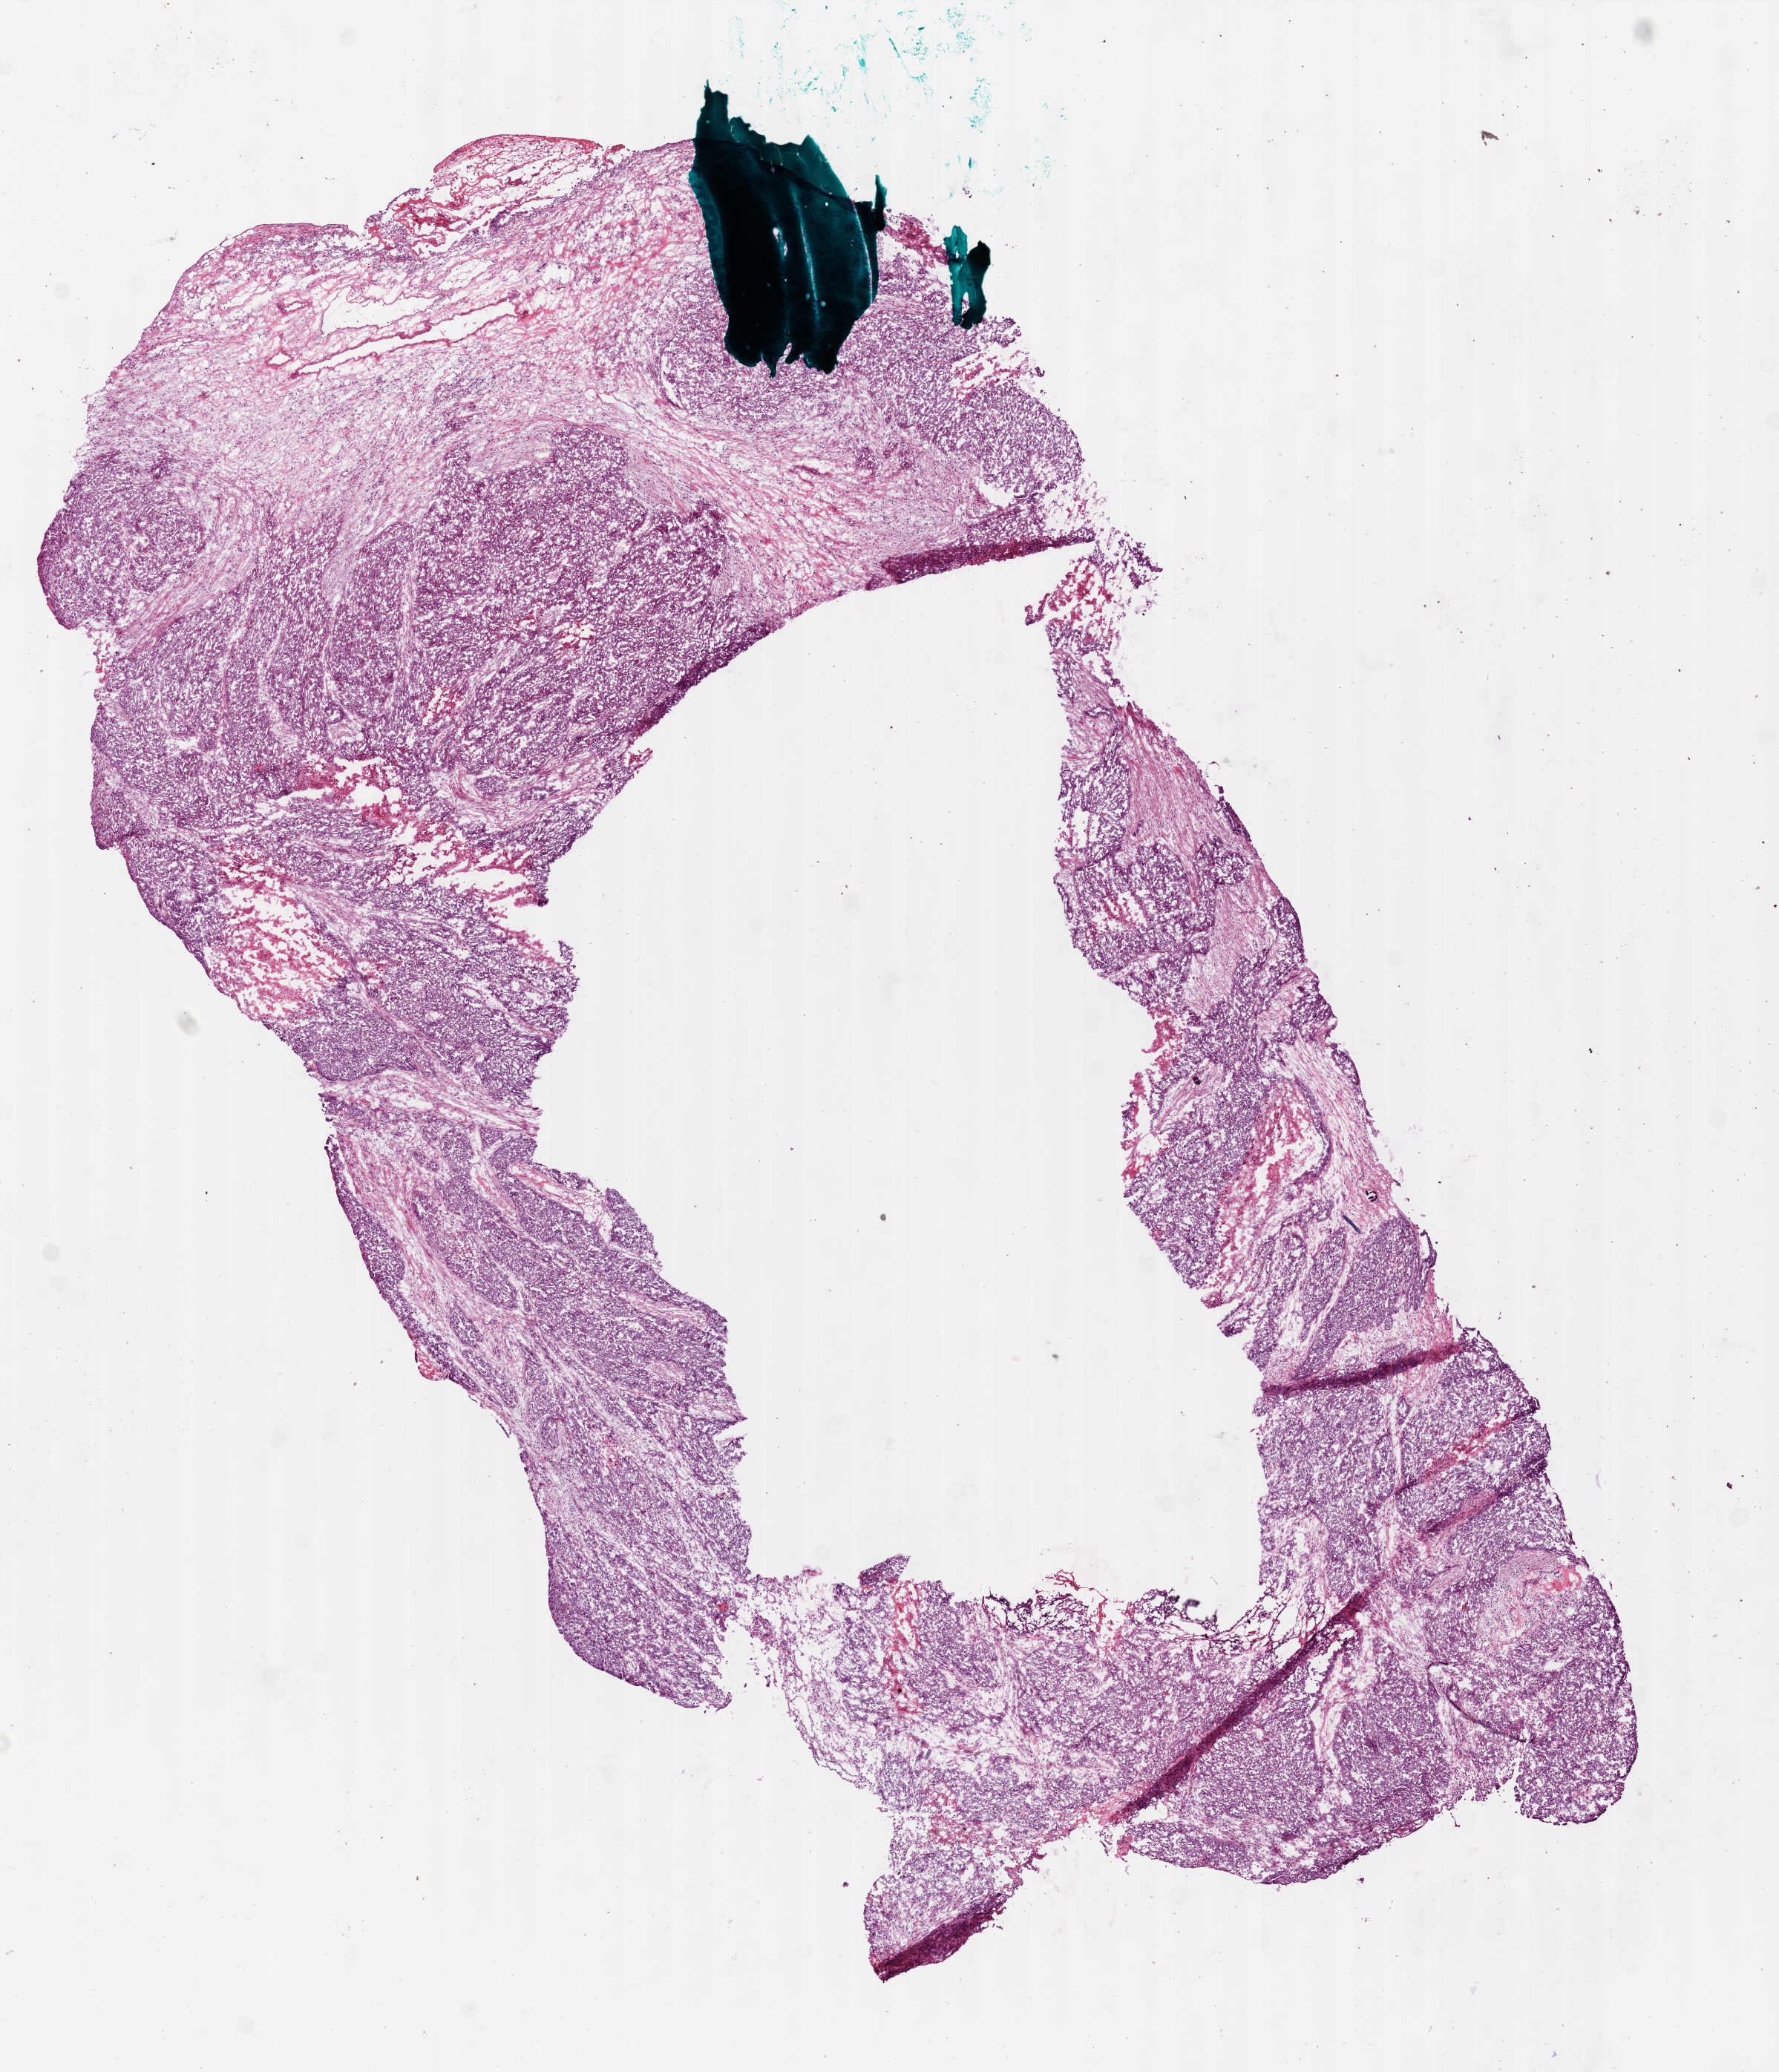
Whole-slide histology image, H&E, whole scanned area (about 9.6 x 11.2 mm, from a 20x scan) shown as a low-resolution overview, frozen section from the bottom of the tissue portion, ovary, primary tumour sample. Female, age 57 years at initial diagnosis. Histologic grade: G3 (poorly differentiated). Pathologist review of this section (percent, as recorded): tumour cells 70%, tumour nuclei 80%, normal cells 0%, stromal cells 30%, necrosis 0%. Infiltration values recorded for this section: lymphocyte infiltration 30%.
• laterality: bilateral
• FIGO stage: IIIC
• histologic diagnosis: Serous cystadenocarcinoma, NOS